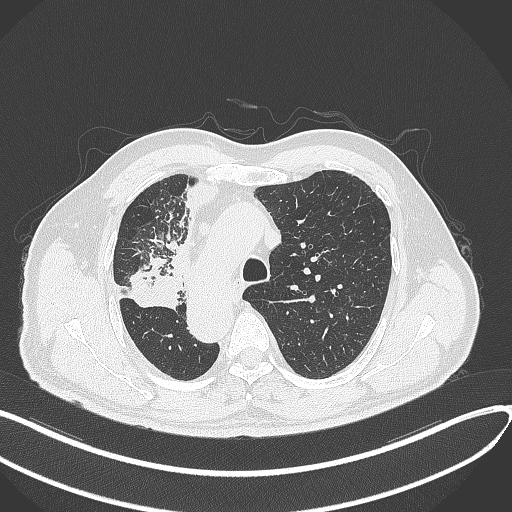
Chest CT, one axial slice; slice 230 of 300 in the series (ordered by position); reconstruction kernel B70f; 120 kVp; lung window (W 1500 / L -600 HU); 1 mm slice thickness; 512 × 512 image matrix, field of view 400 × 400 mm. Patient: male, 67 years. From the clinical record (not read from this slice): clinical TNM (as recorded): T2a N0 M0.
Annotated regions visible in this slice (bounding box drawn by a radiologist):
- lung tumour (recorded histology: squamous cell carcinoma): bounding box [x1, y1, x2, y2] px = [127, 254, 186, 313]